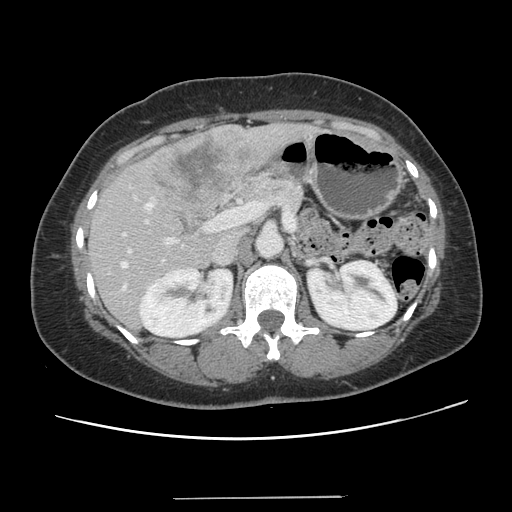
Contrast-enhanced abdominal CT, one axial slice. Slice 68 of 141 in the series (ordered by position). 120 kVp. Intravenous contrast given. Soft-tissue window (W 400 / L 40 HU). 512 × 512 image matrix. Female patient, age 53 years. From the clinical record (not read from this slice): diagnosis: colorectal cancer liver metastases, imaged before liver resection.
Structures marked on this image (expert manual segmentation):
- hepatic veins: bounding box [x1, y1, x2, y2] px = [121, 249, 130, 289]
- liver: [90, 125, 307, 329]
- planned liver remnant (the part of the liver to remain after resection): [90, 209, 247, 330]
- portal vein (with intrahepatic branches): [123, 202, 218, 244]
- liver metastasis: [152, 135, 251, 203]